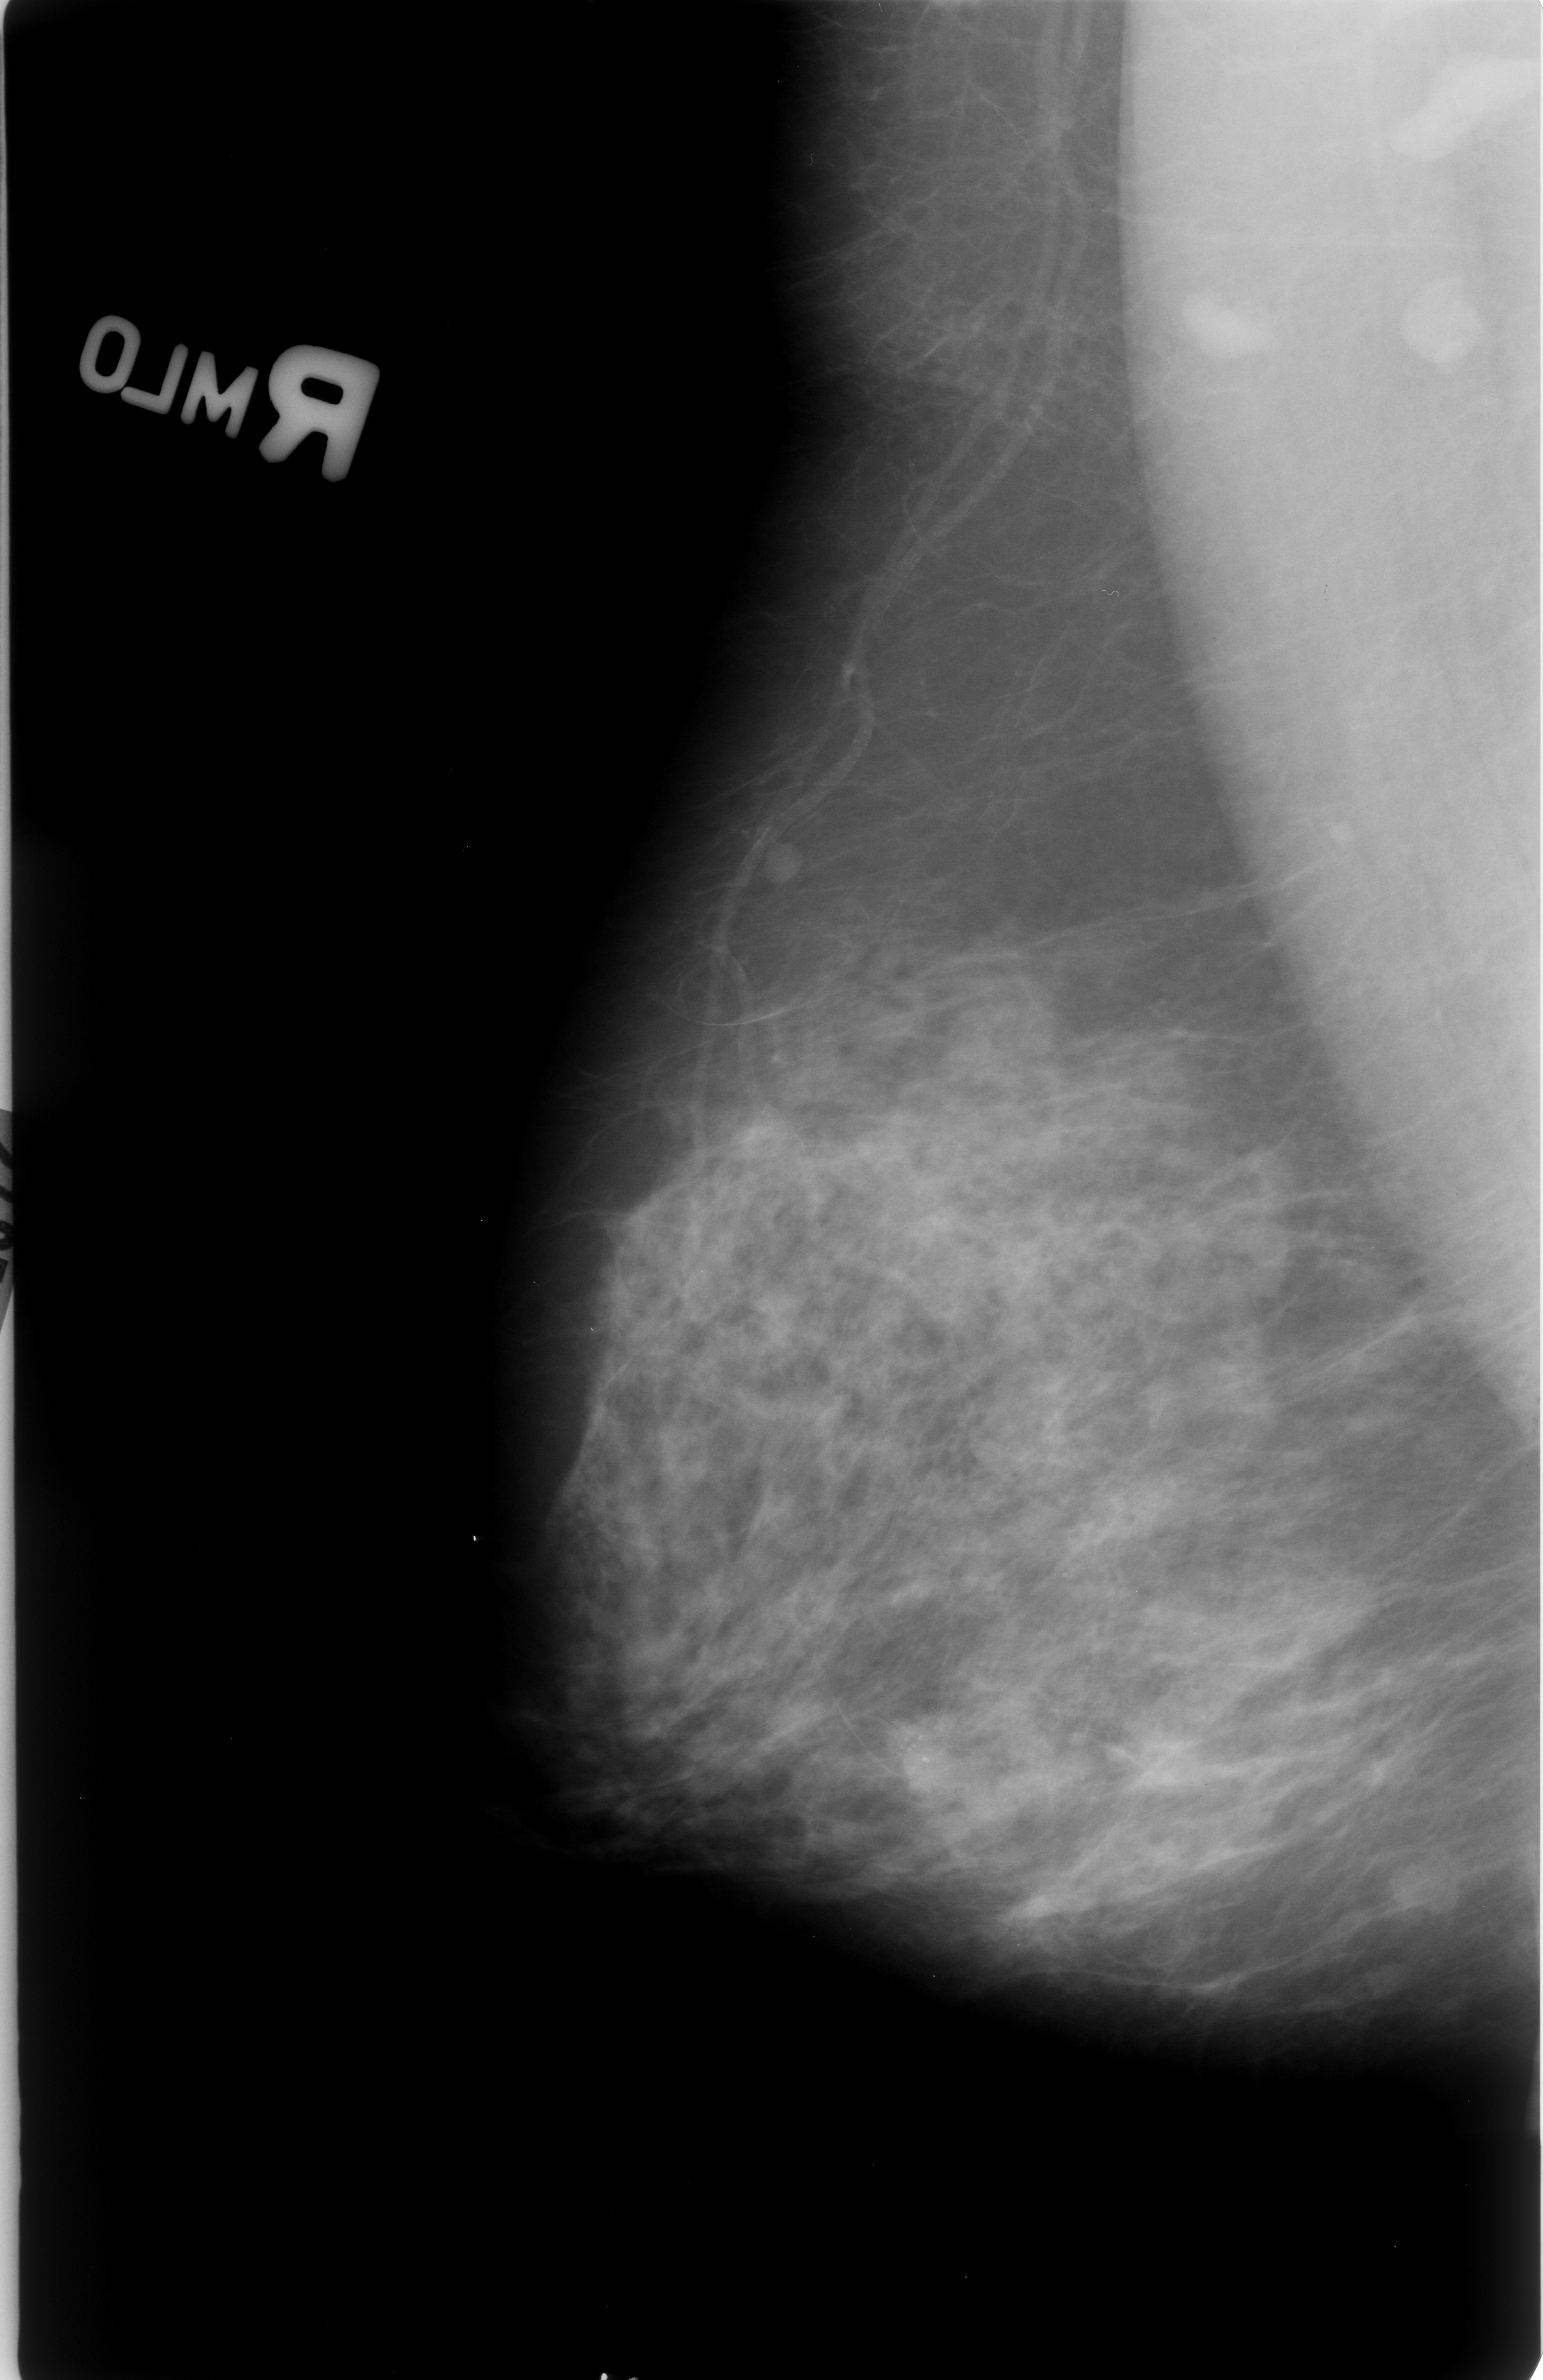
Scanned film-screen mammogram; right breast; MLO view; breast composition: heterogeneously dense (BI-RADS density category 3 of 4).
Finding: calcifications, morphology pleomorphic, distribution clustered; BI-RADS assessment category 4; pathology (as recorded): malignant.